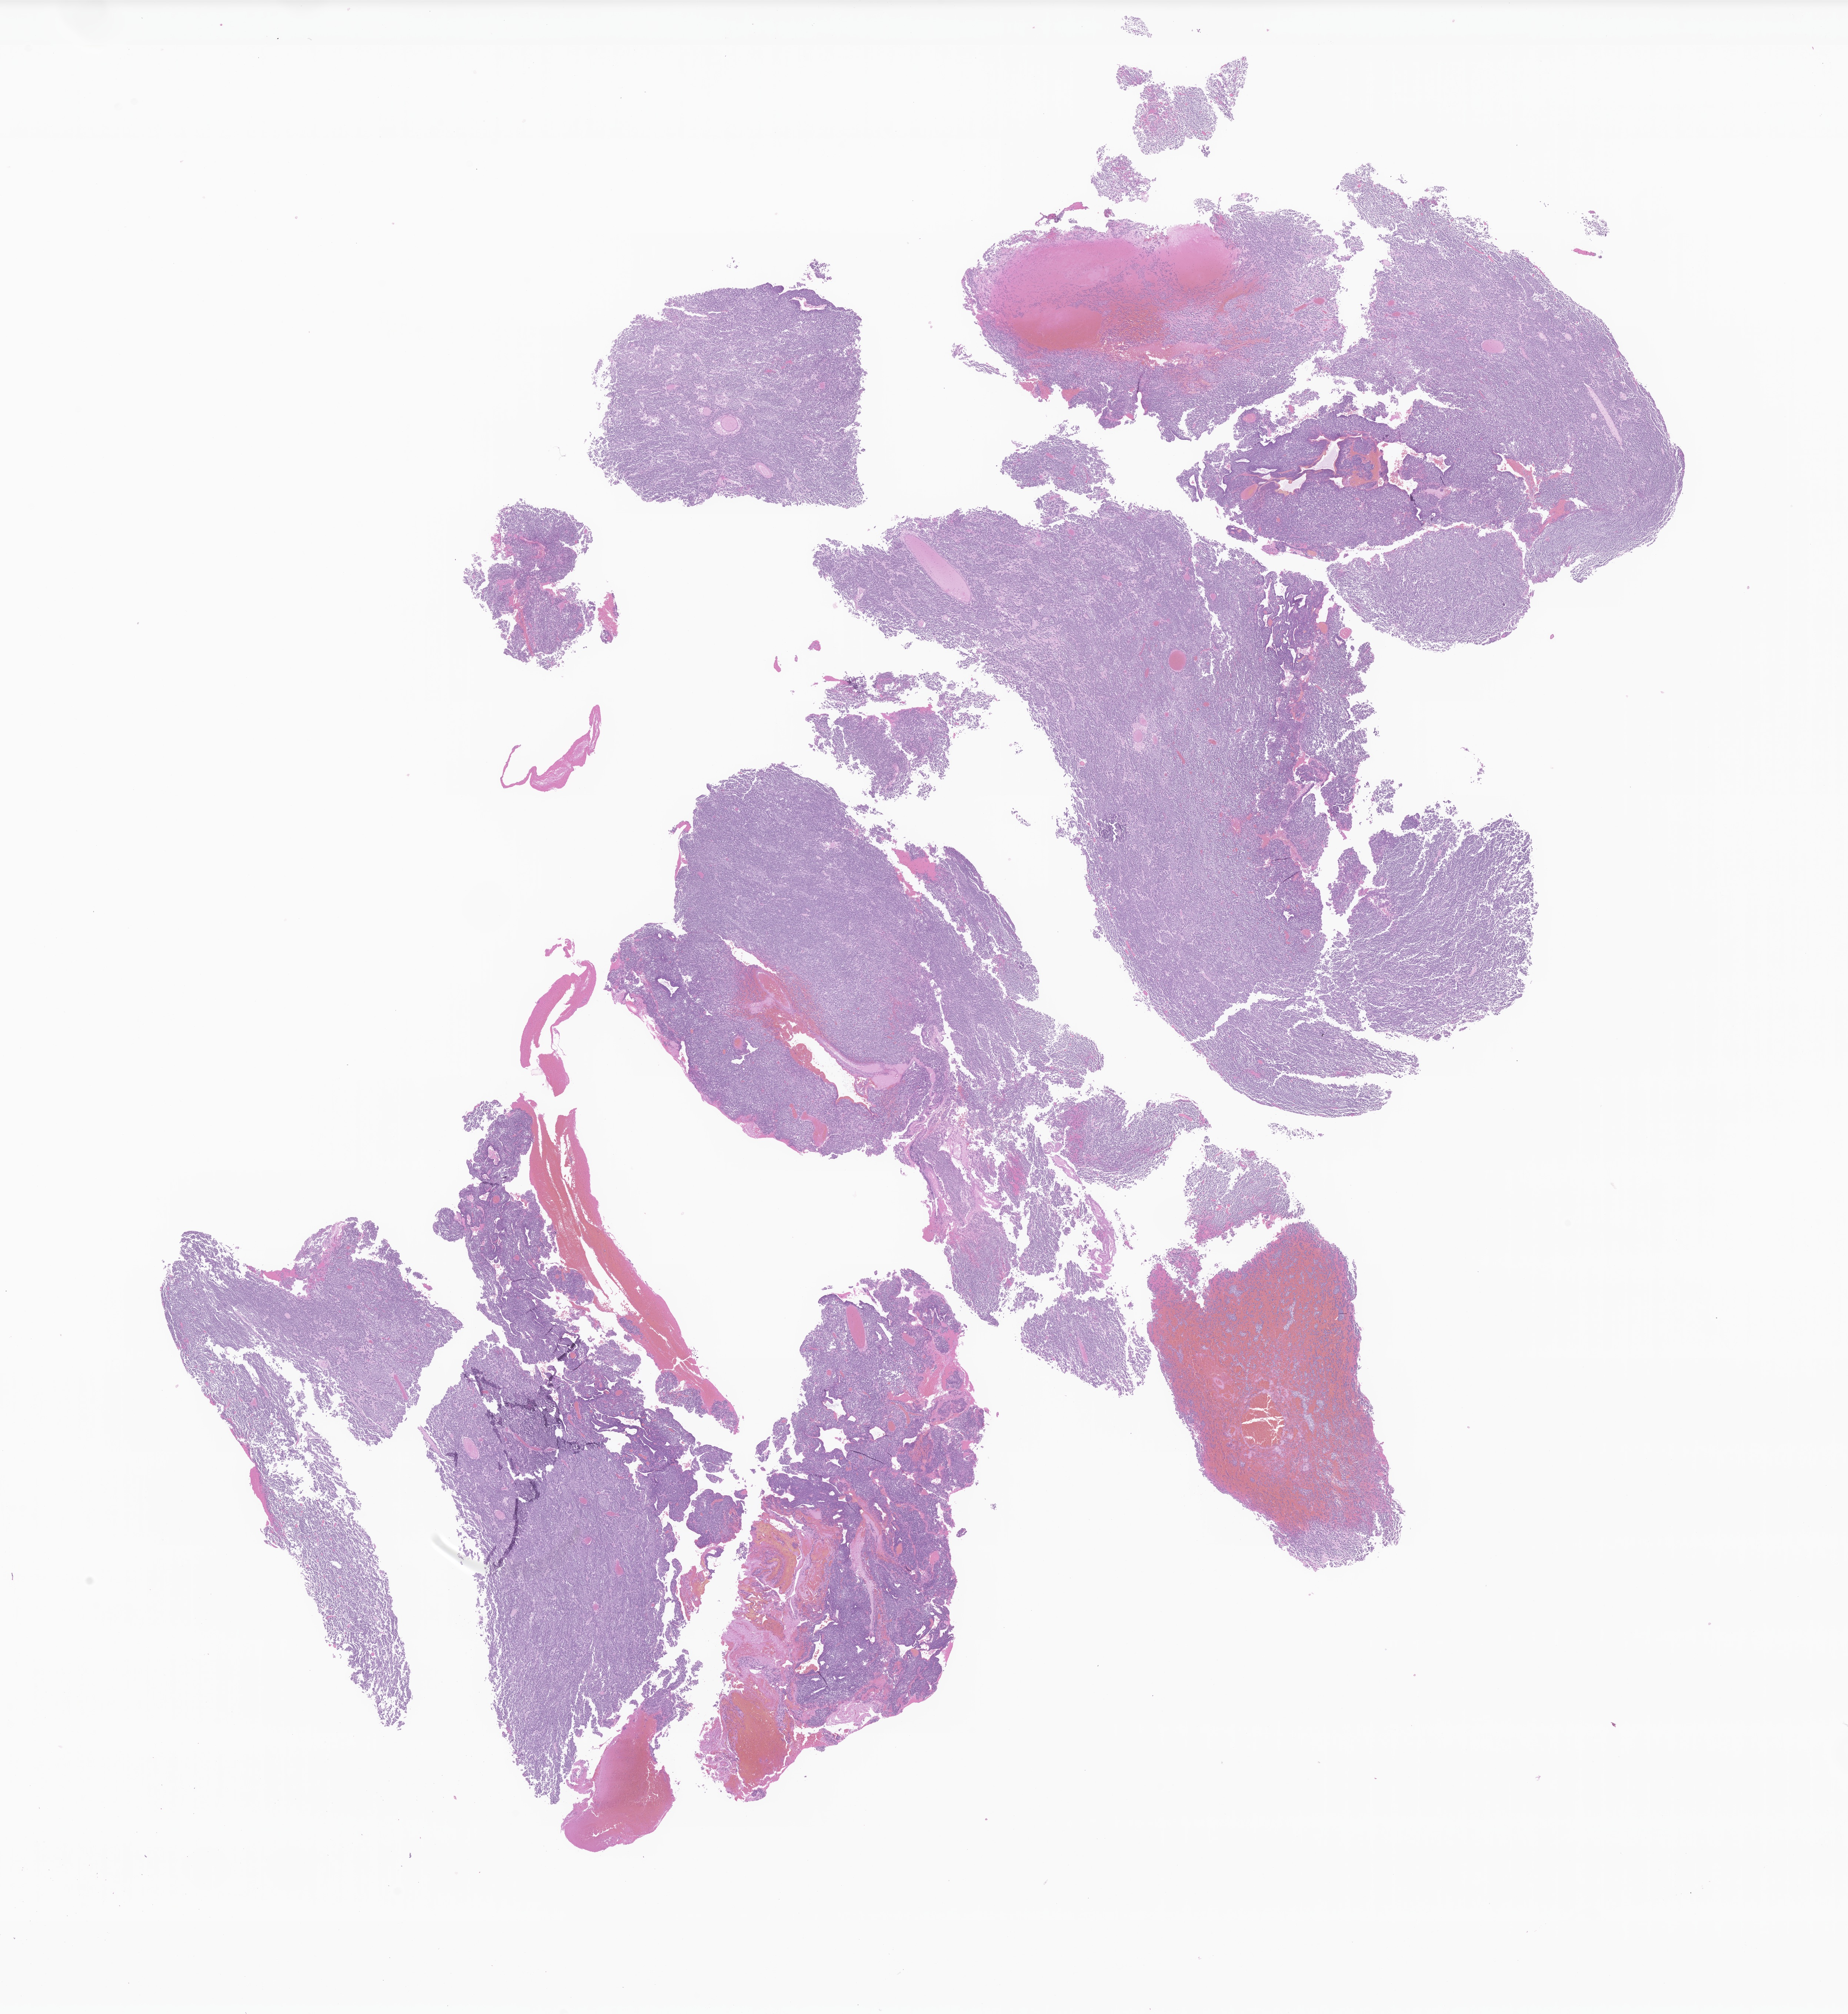
Whole-slide image, H&E stain of tumor tissue from the brain — shown as a low-resolution overview of the whole scanned area (about 21.0 x 22.9 mm); FFPE section. Male patient, age 256 months (21 years 4 months).
Recorded diagnosis: Medulloblastoma, NOS.